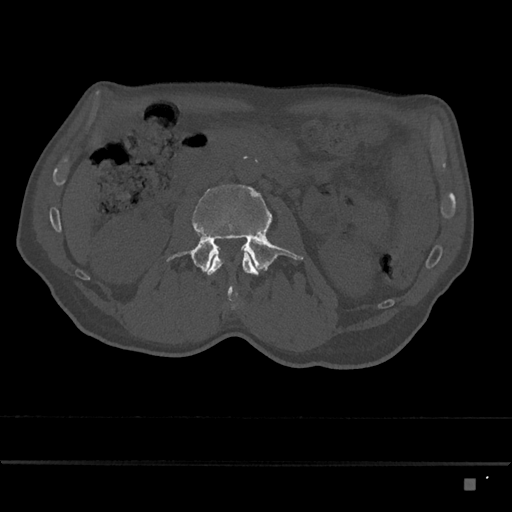
CT including the spine, one axial slice; slice 430 of 797 in the series (ordered by position); 120 kVp; bone window (W 1800 / L 400 HU); 0.5 mm slice thickness; 512 × 512 image matrix. Patient: male, 72 years. From the clinical record (not read from this slice): primary cancer: prostate.
Structures marked on this image (semi-automatic segmentation, software-assisted and operator-edited):
- L2 vertebra: box from (x=204, y=253) to (x=258, y=310) px
- L3 vertebra: (x=167, y=184)–(x=303, y=274)